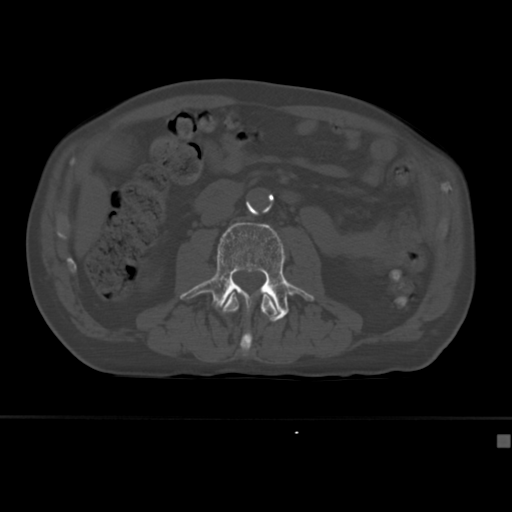
CT including the spine, one axial slice; slice 133 of 430 in the series (ordered by position); bone window (W 1800 / L 400 HU); 1.5 mm slice thickness; 512 × 512 image matrix, field of view 337 × 337 mm. Male patient, age 64 years. From the clinical record (not read from this slice): primary cancer: uterus; vertebrae with lytic lesions (as recorded): T1, T4, T5, T7, L5.
Annotated regions visible in this slice (semi-automatic segmentation, software-assisted and operator-edited):
- L2 vertebra: bounding box [x1, y1, x2, y2] px = [222, 292, 280, 357]
- L3 vertebra: [180, 222, 314, 322]